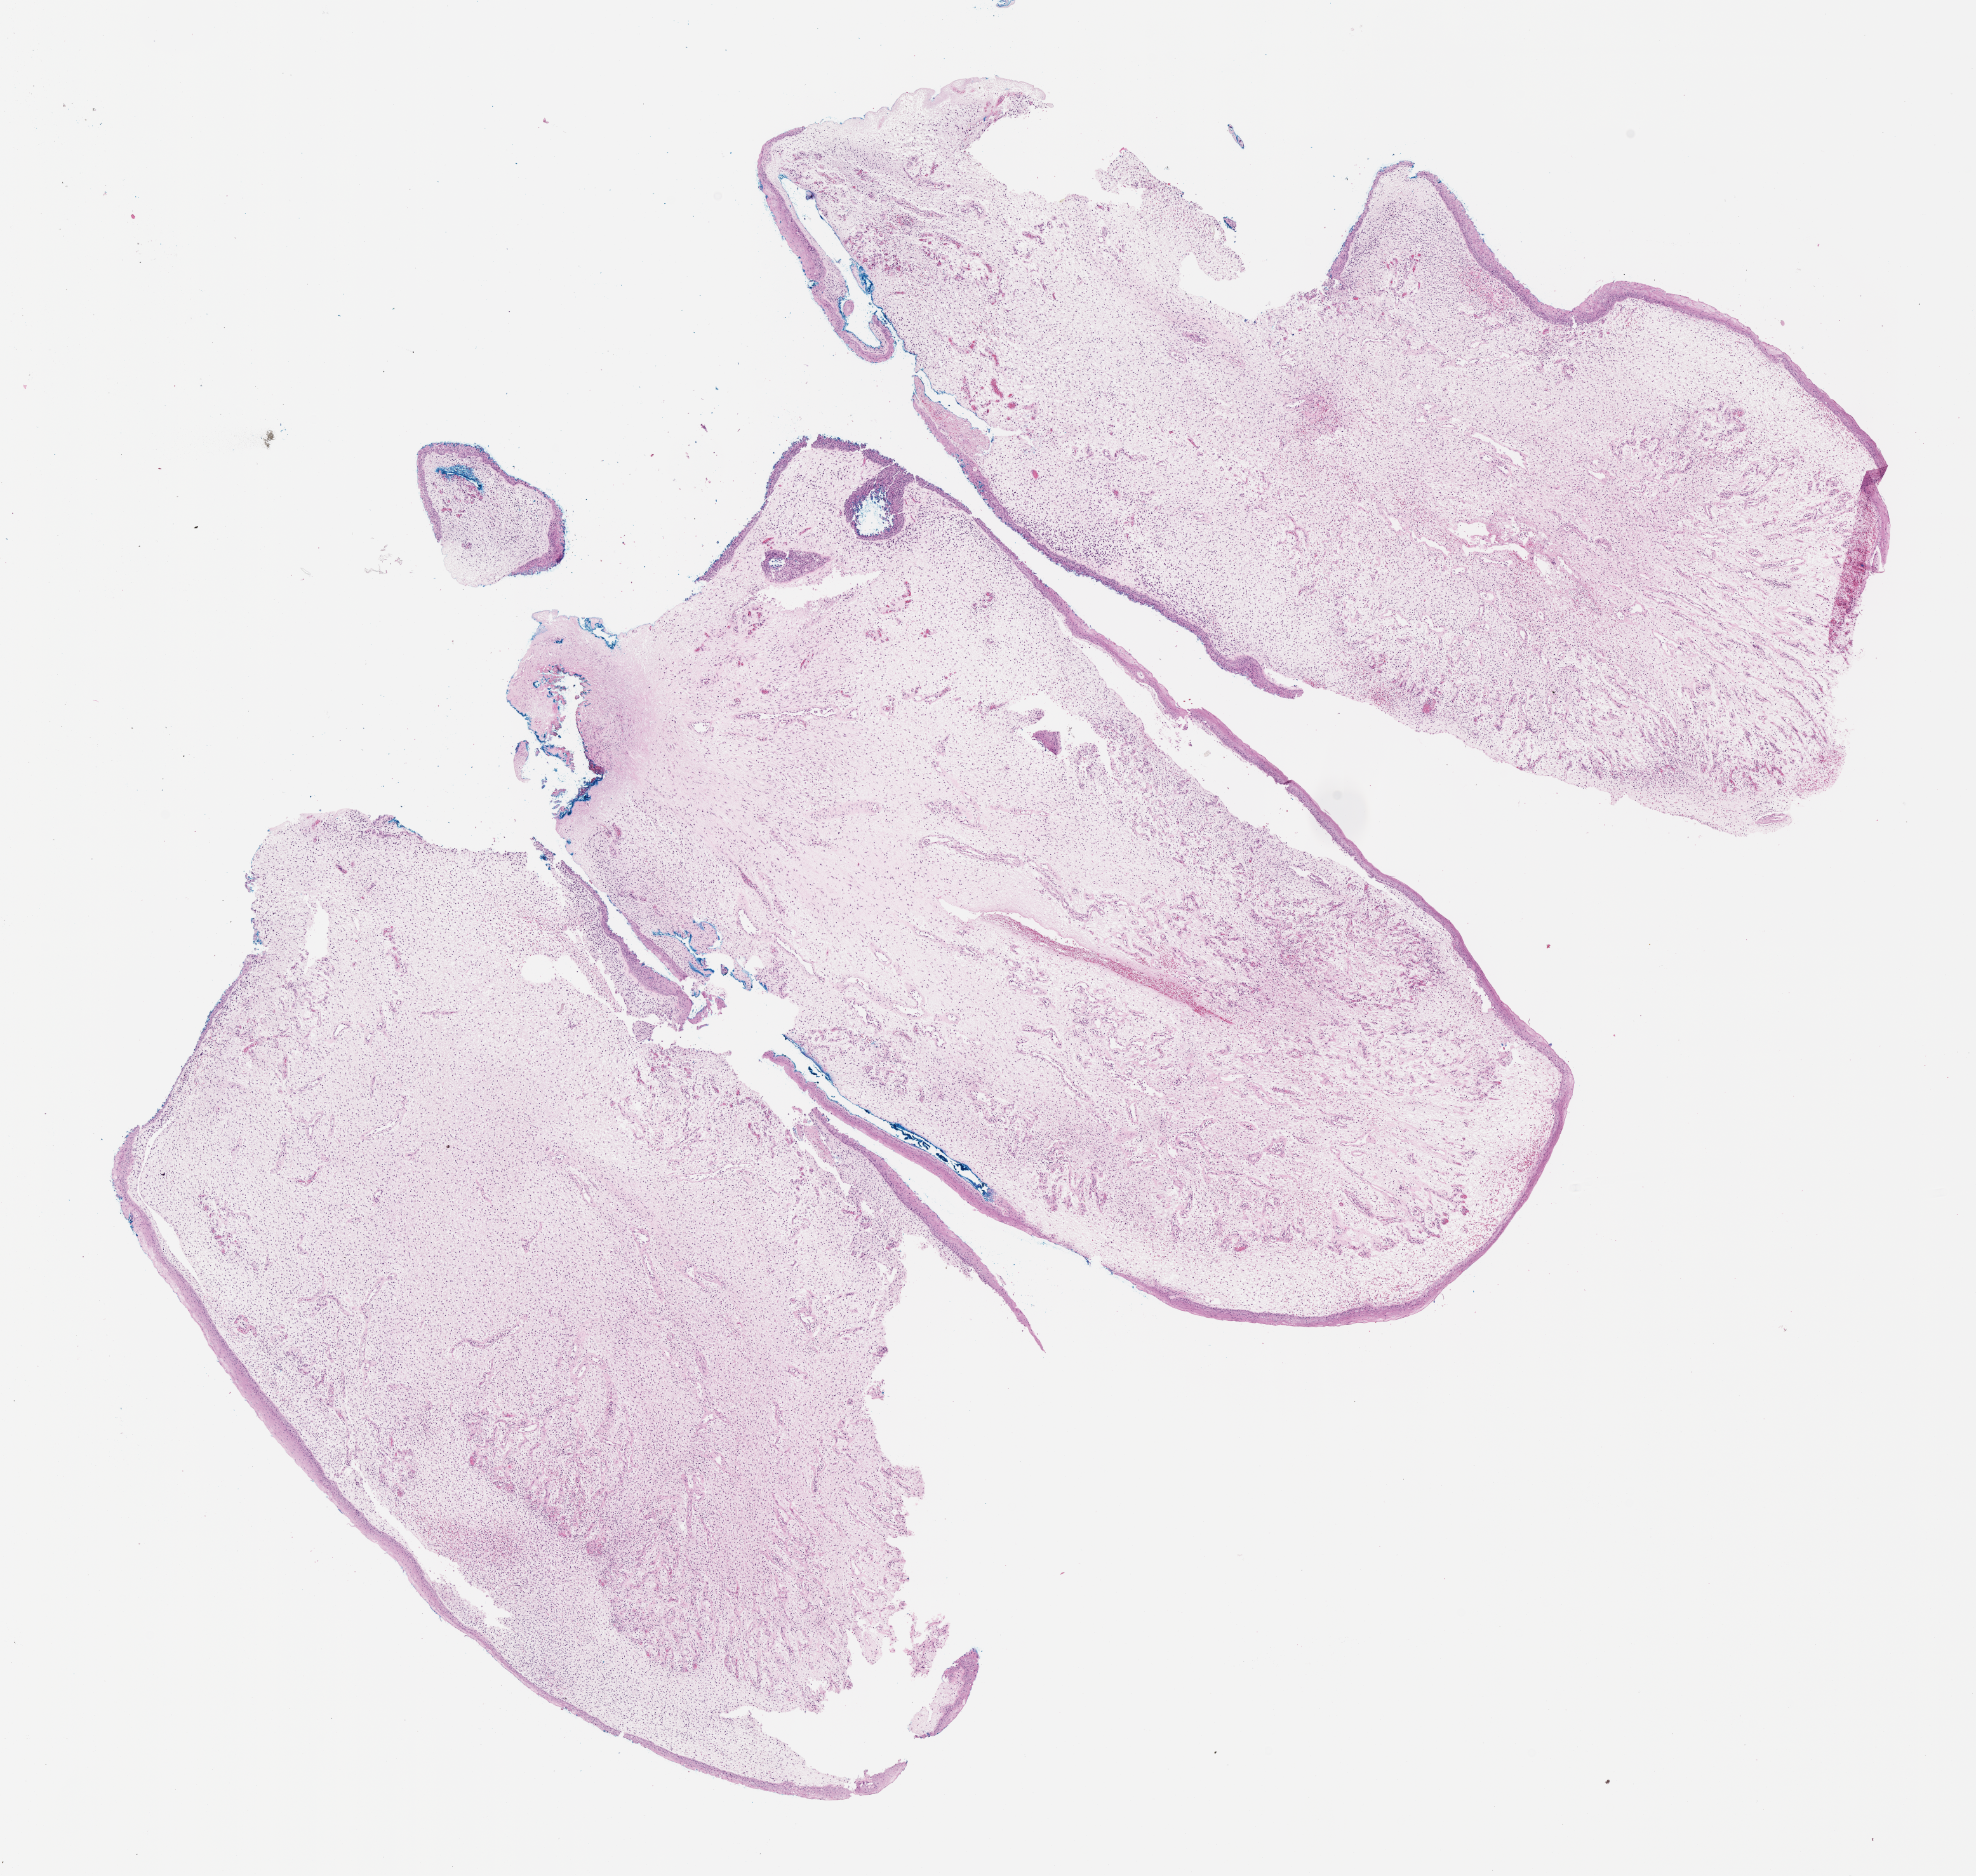
Haematoxylin and eosin whole-slide image of tumor tissue, a low-resolution overview of the entire scanned area, about 12.6 x 11.9 mm, formalin-fixed paraffin-embedded section. Patient: male, age 0.8 years at diagnosis.
Diagnosis: rhabdomyosarcoma; histological classification: botryoid. Metastatic status at presentation (as recorded): non-metastatic. Stage (as recorded): 2.